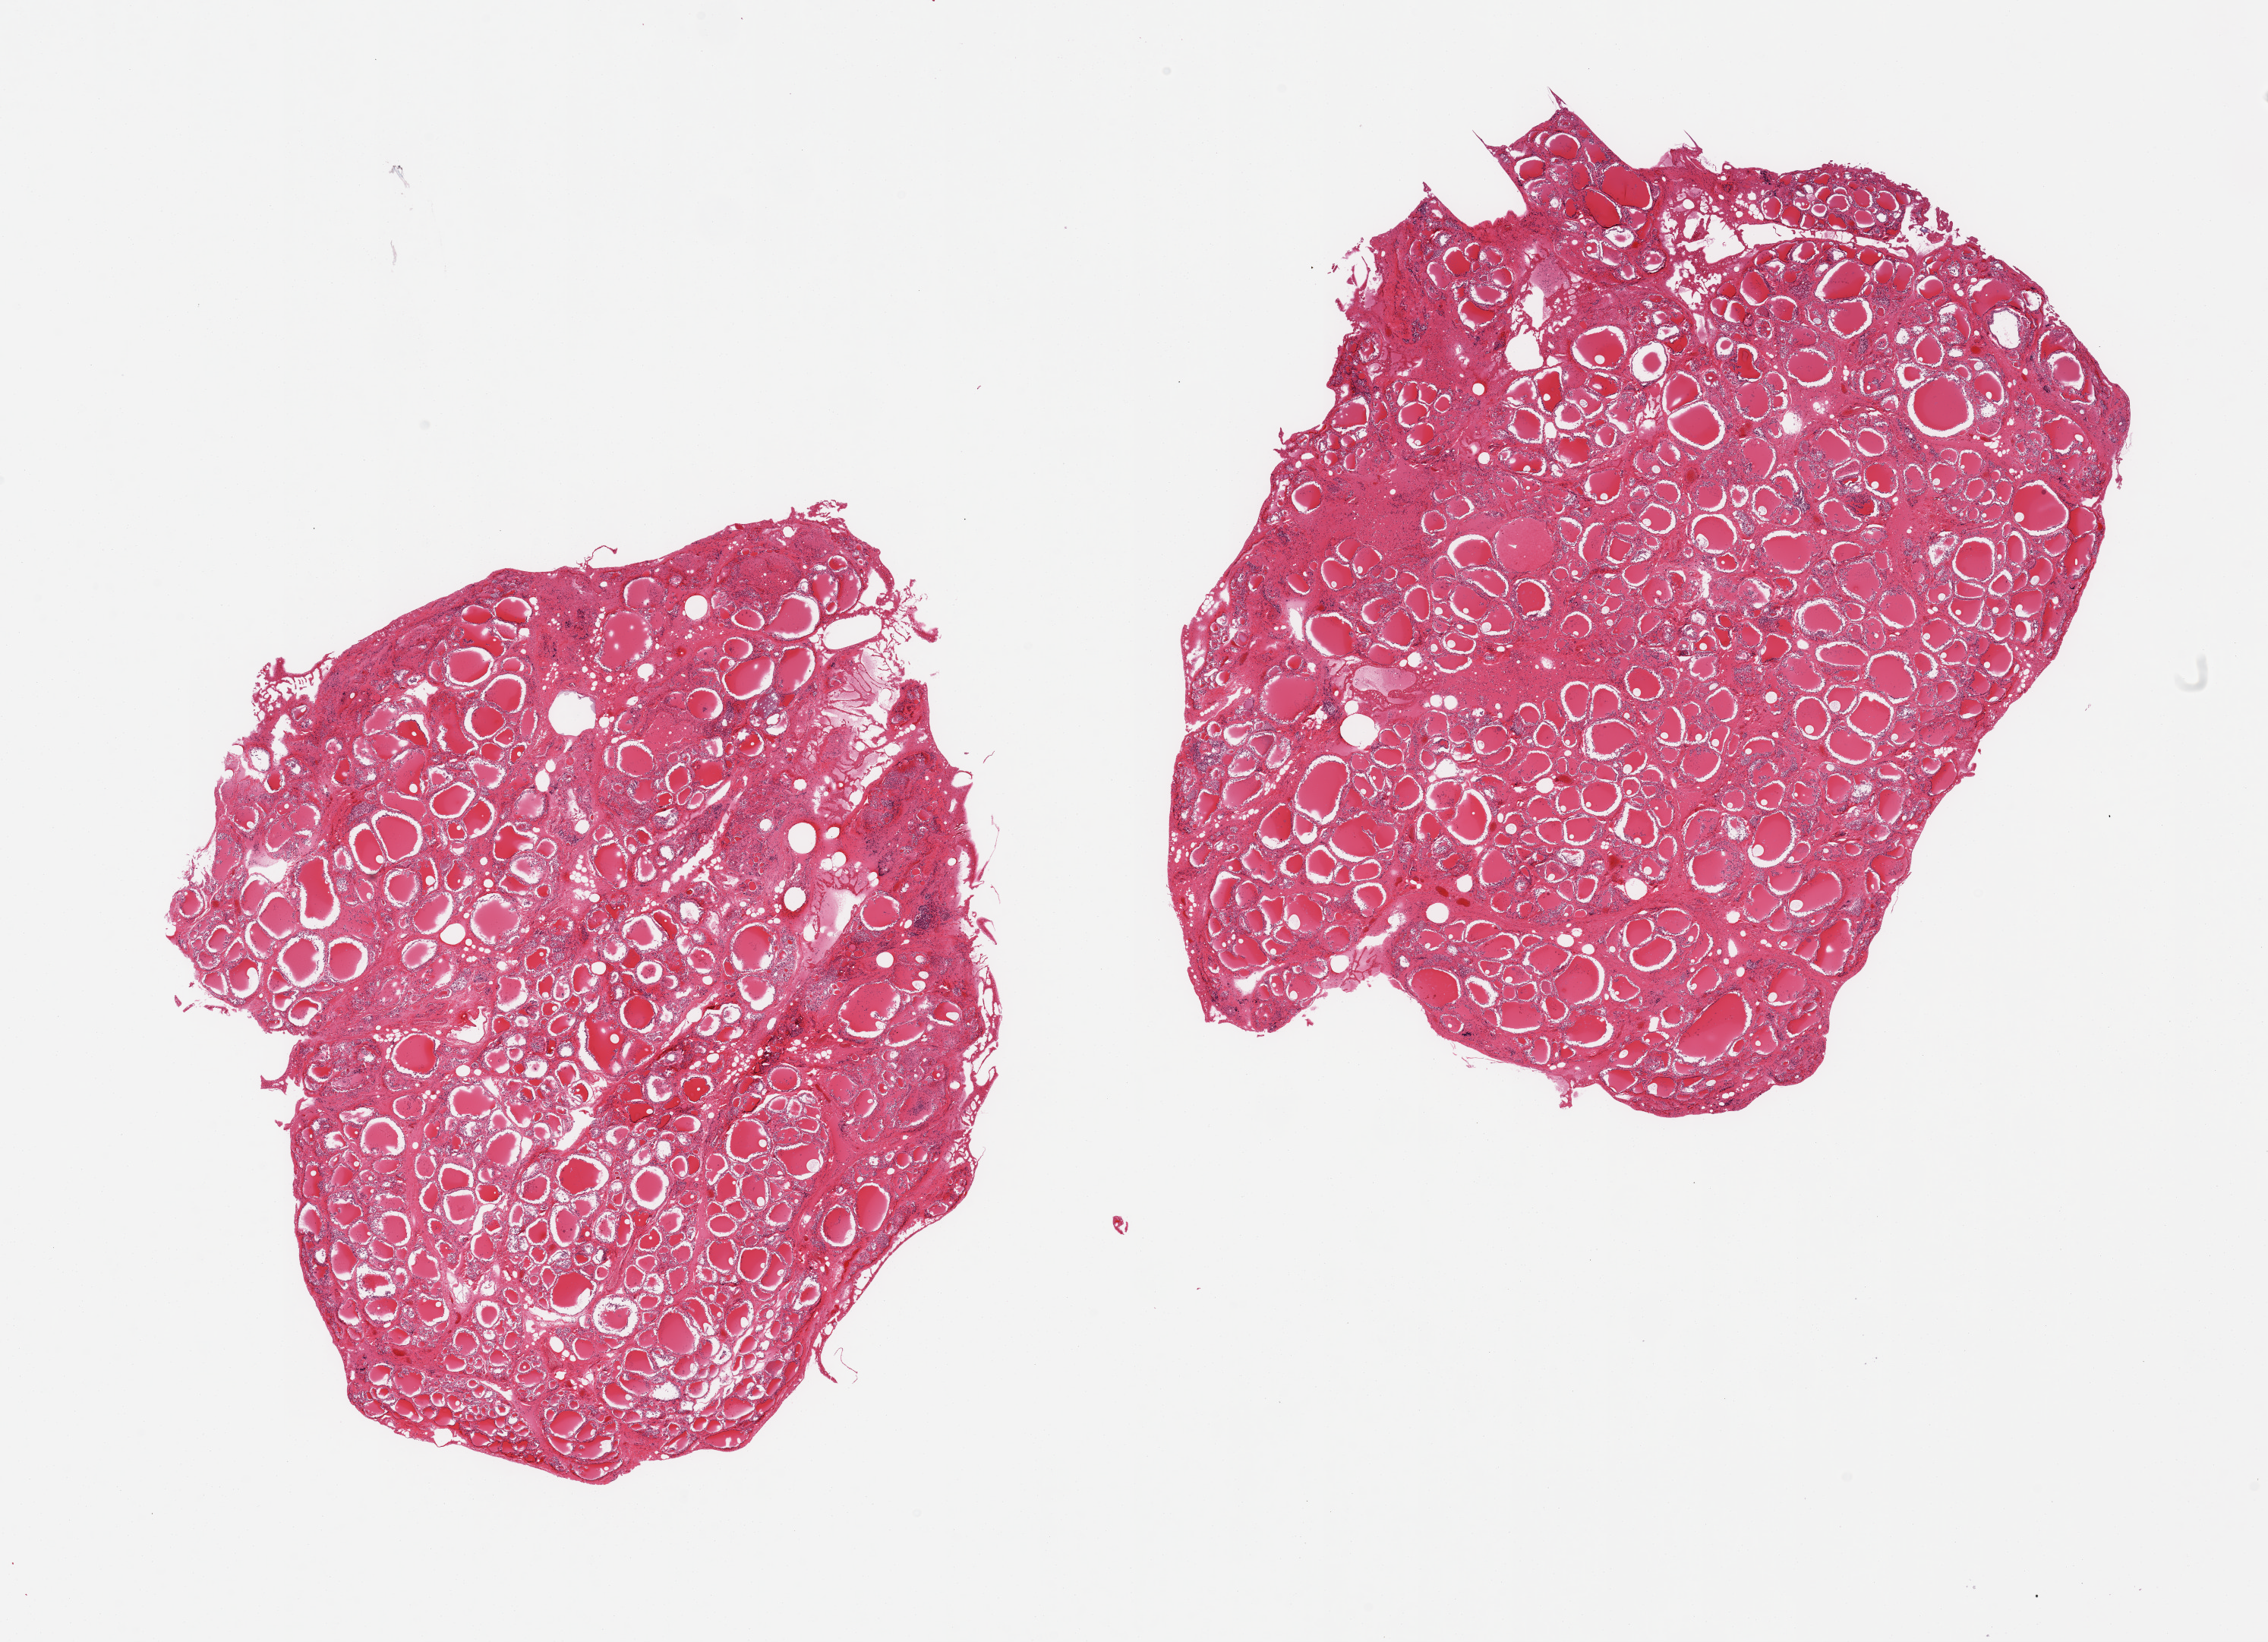
Whole-slide image, H&E stain — a low-resolution overview of the entire scanned area, about 23.6 x 17.1 mm, PAXgene-fixed paraffin-embedded (PFPE) section, section of thyroid (target tissue), tissue donor sample. Donor: male.
Review note (as recorded): 2 pieces, moderately advanced autolysis, no abnormalities.